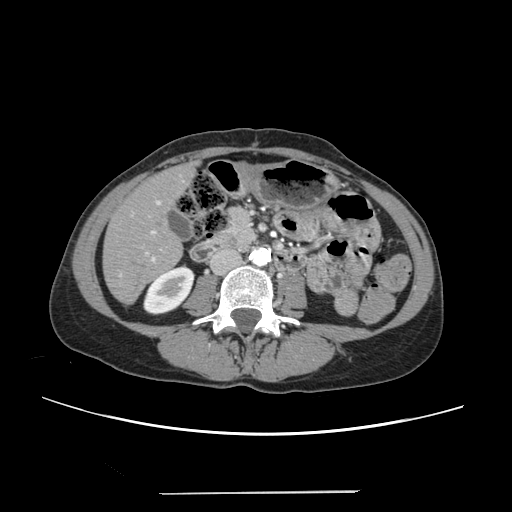
Contrast-enhanced abdominal CT, one axial slice; slice 76 of 240 in the series (ordered by position); 120 kVp; soft-tissue window (W 400 / L 40 HU); 512 × 512 image matrix. Female patient, age 60 years. Case-level facts recorded for this patient, not image findings: diagnosis: colorectal cancer liver metastases, imaged before liver resection; multiple liver metastases: no; largest metastasis: 1.5 cm; disease in both lobes: no.
Annotated regions visible in this slice (outlined manually by an expert reader):
- liver: bounding box [x1, y1, x2, y2] px = [105, 165, 194, 303]
- planned liver remnant (the part of the liver to remain after resection): [105, 172, 181, 303]
- portal vein (with intrahepatic branches): [132, 201, 162, 261]